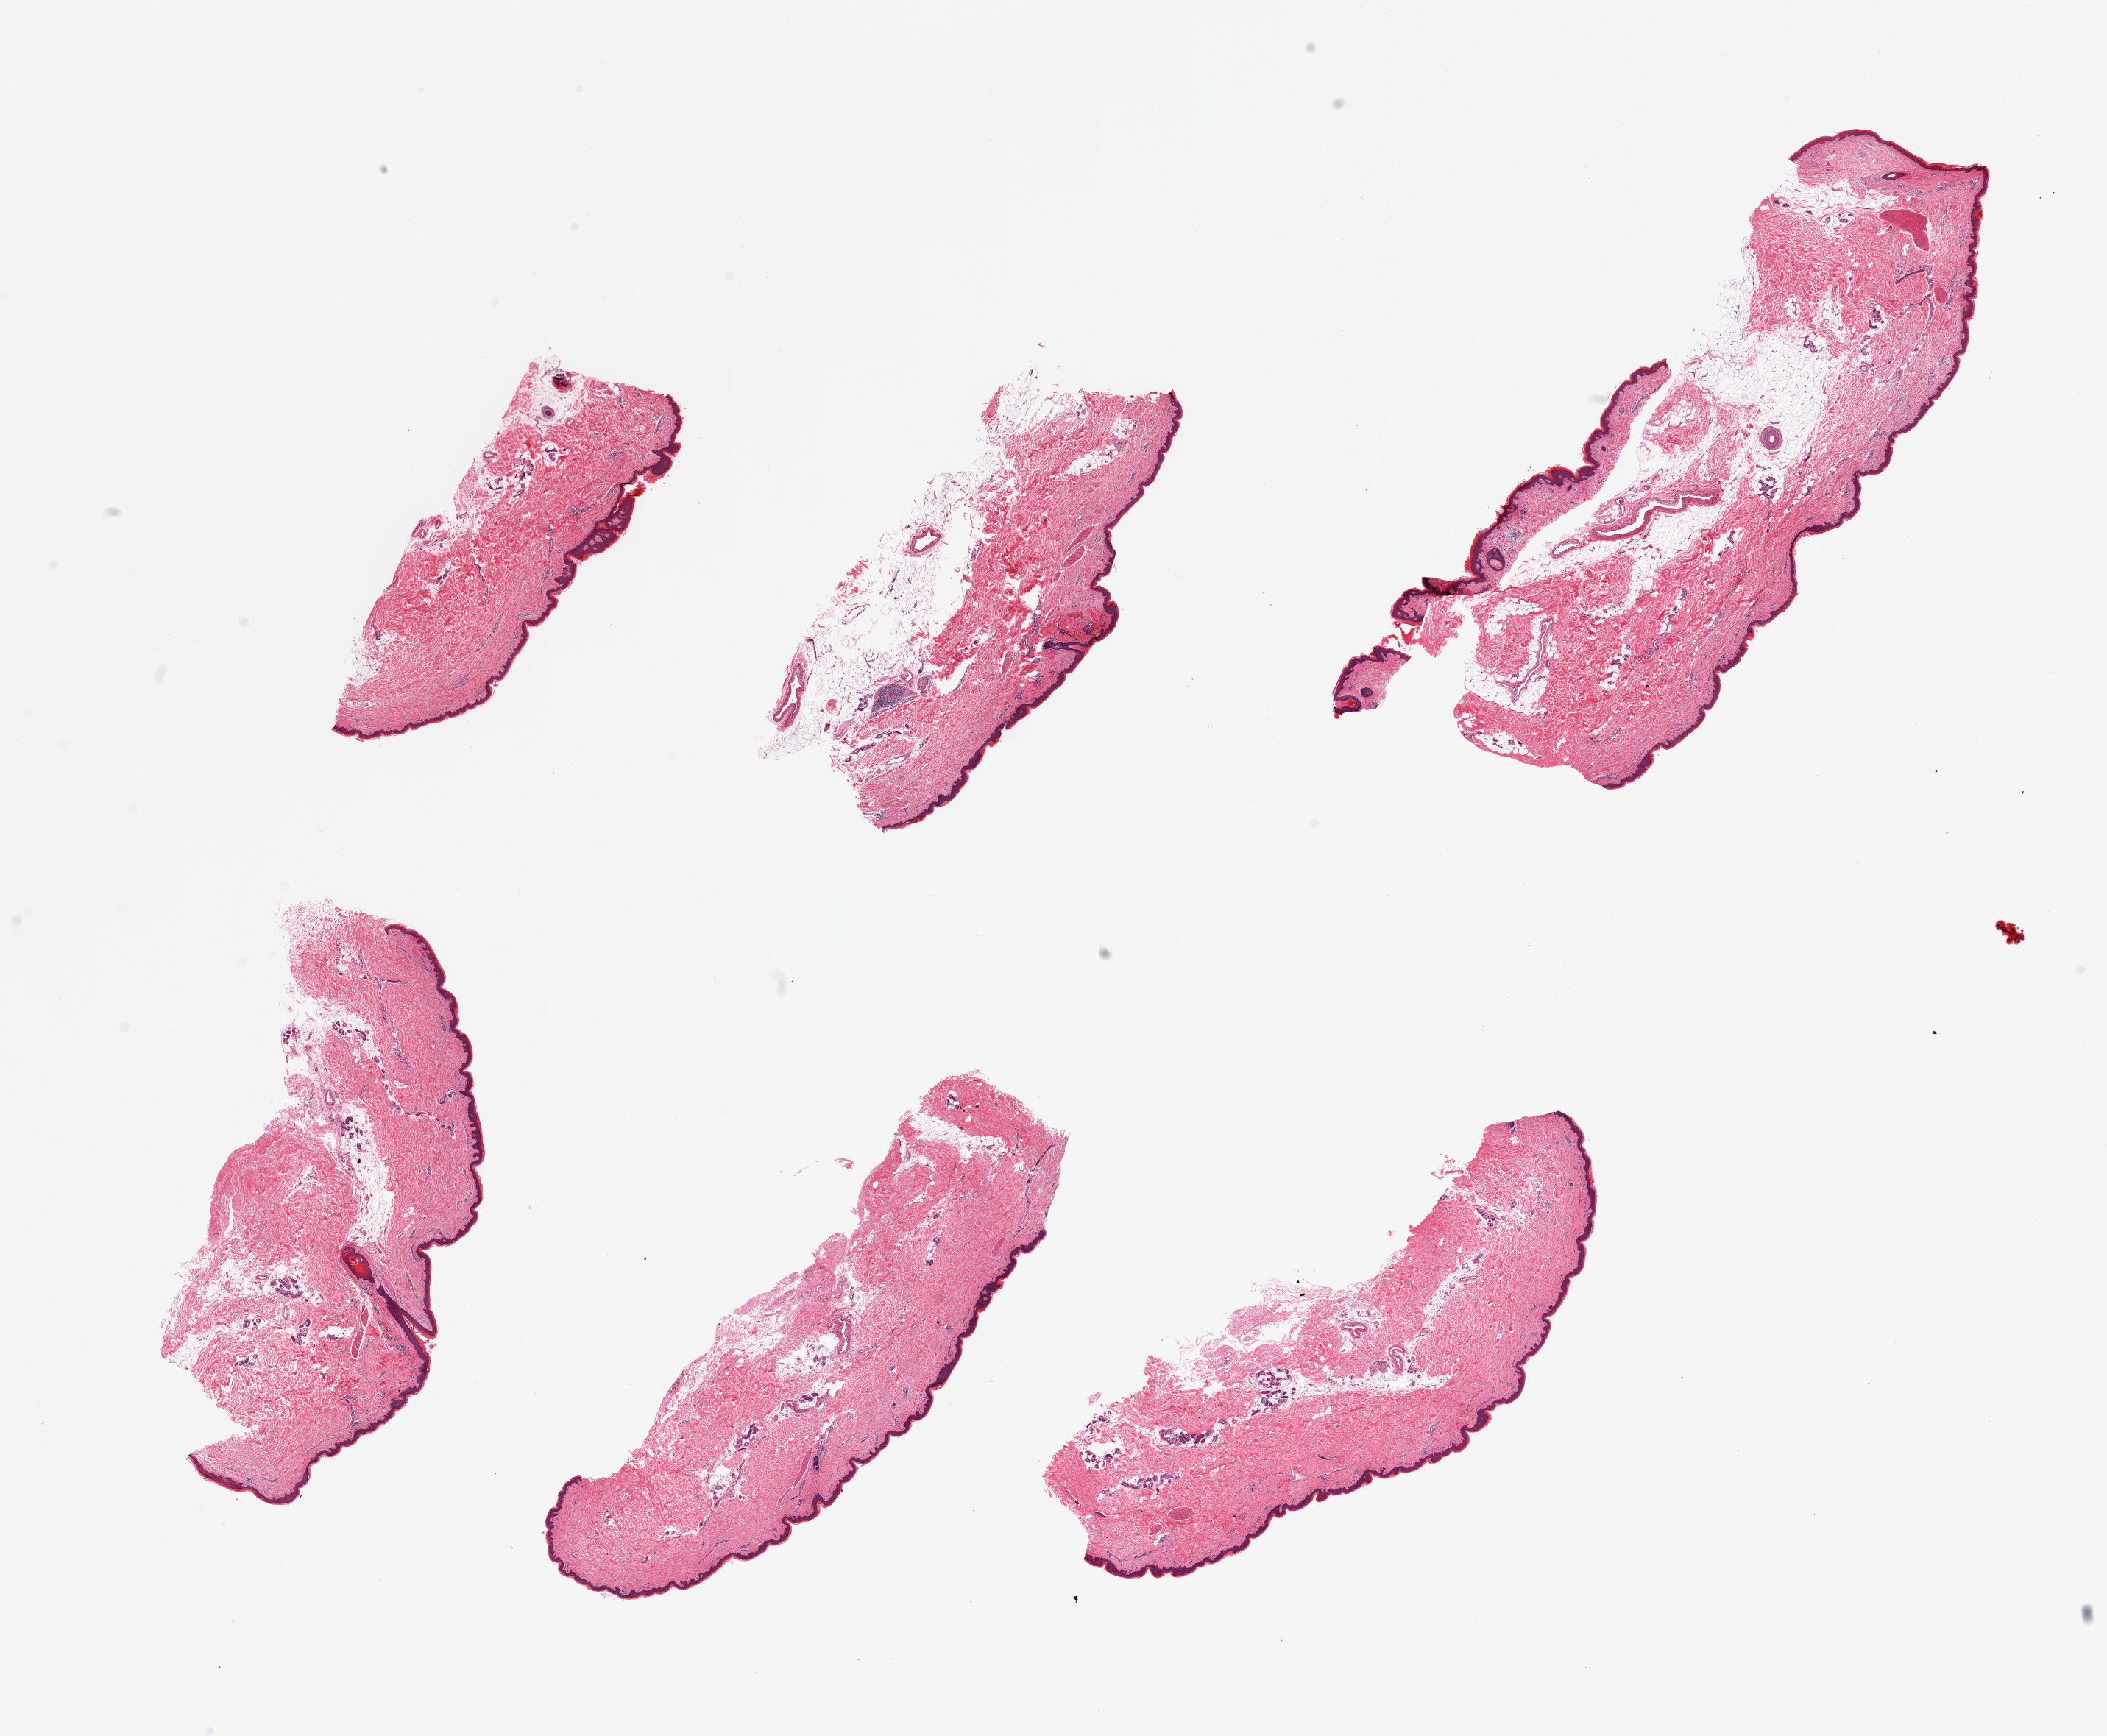
H&E whole-slide image — whole scanned area (about 22.6 x 18.7 mm, from a 20x scan) shown as a low-resolution overview. PAXgene-fixed, paraffin-embedded tissue. Section of skin of lower leg (target tissue). Donor tissue sample. Female donor.
* review note (as recorded): 6 pieces, minimal dermal fat, squamous epithelium is ~50-60 microns